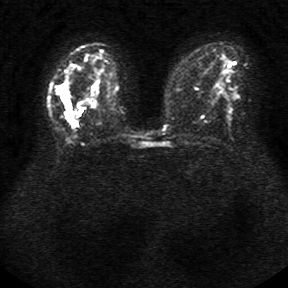
Breast MRI, one axial slice; diffusion-weighted series; image 2 of 4 stored at this slice position (different b-values; order by instance number); 1.5 T; 5 mm slice thickness; 288 × 288 image matrix, field of view 340 × 340 mm. Female patient.
Structures marked on this image (expert manual segmentation):
- tumour on diffusion-weighted imaging: bounding box <76,82,99,117> (left, top, right, bottom; pixels)